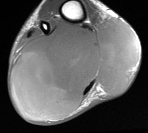
MRI of an extremity soft-tissue mass, one axial slice; MR volume resampled by the dataset authors to the PET/CT grid (not the native acquisition matrix); 3.27 mm slice thickness; 148 × 133 image matrix. Male patient. From the clinical record (not read from this slice): histological type: liposarcoma - round cell; grade: high; site of the primary tumour: right calf.
Outlined on this slice (expert contour drawn on MRI and transferred to this co-registered scan by the dataset authors):
- gross tumour volume (mass): box from (x=13, y=19) to (x=139, y=116) px